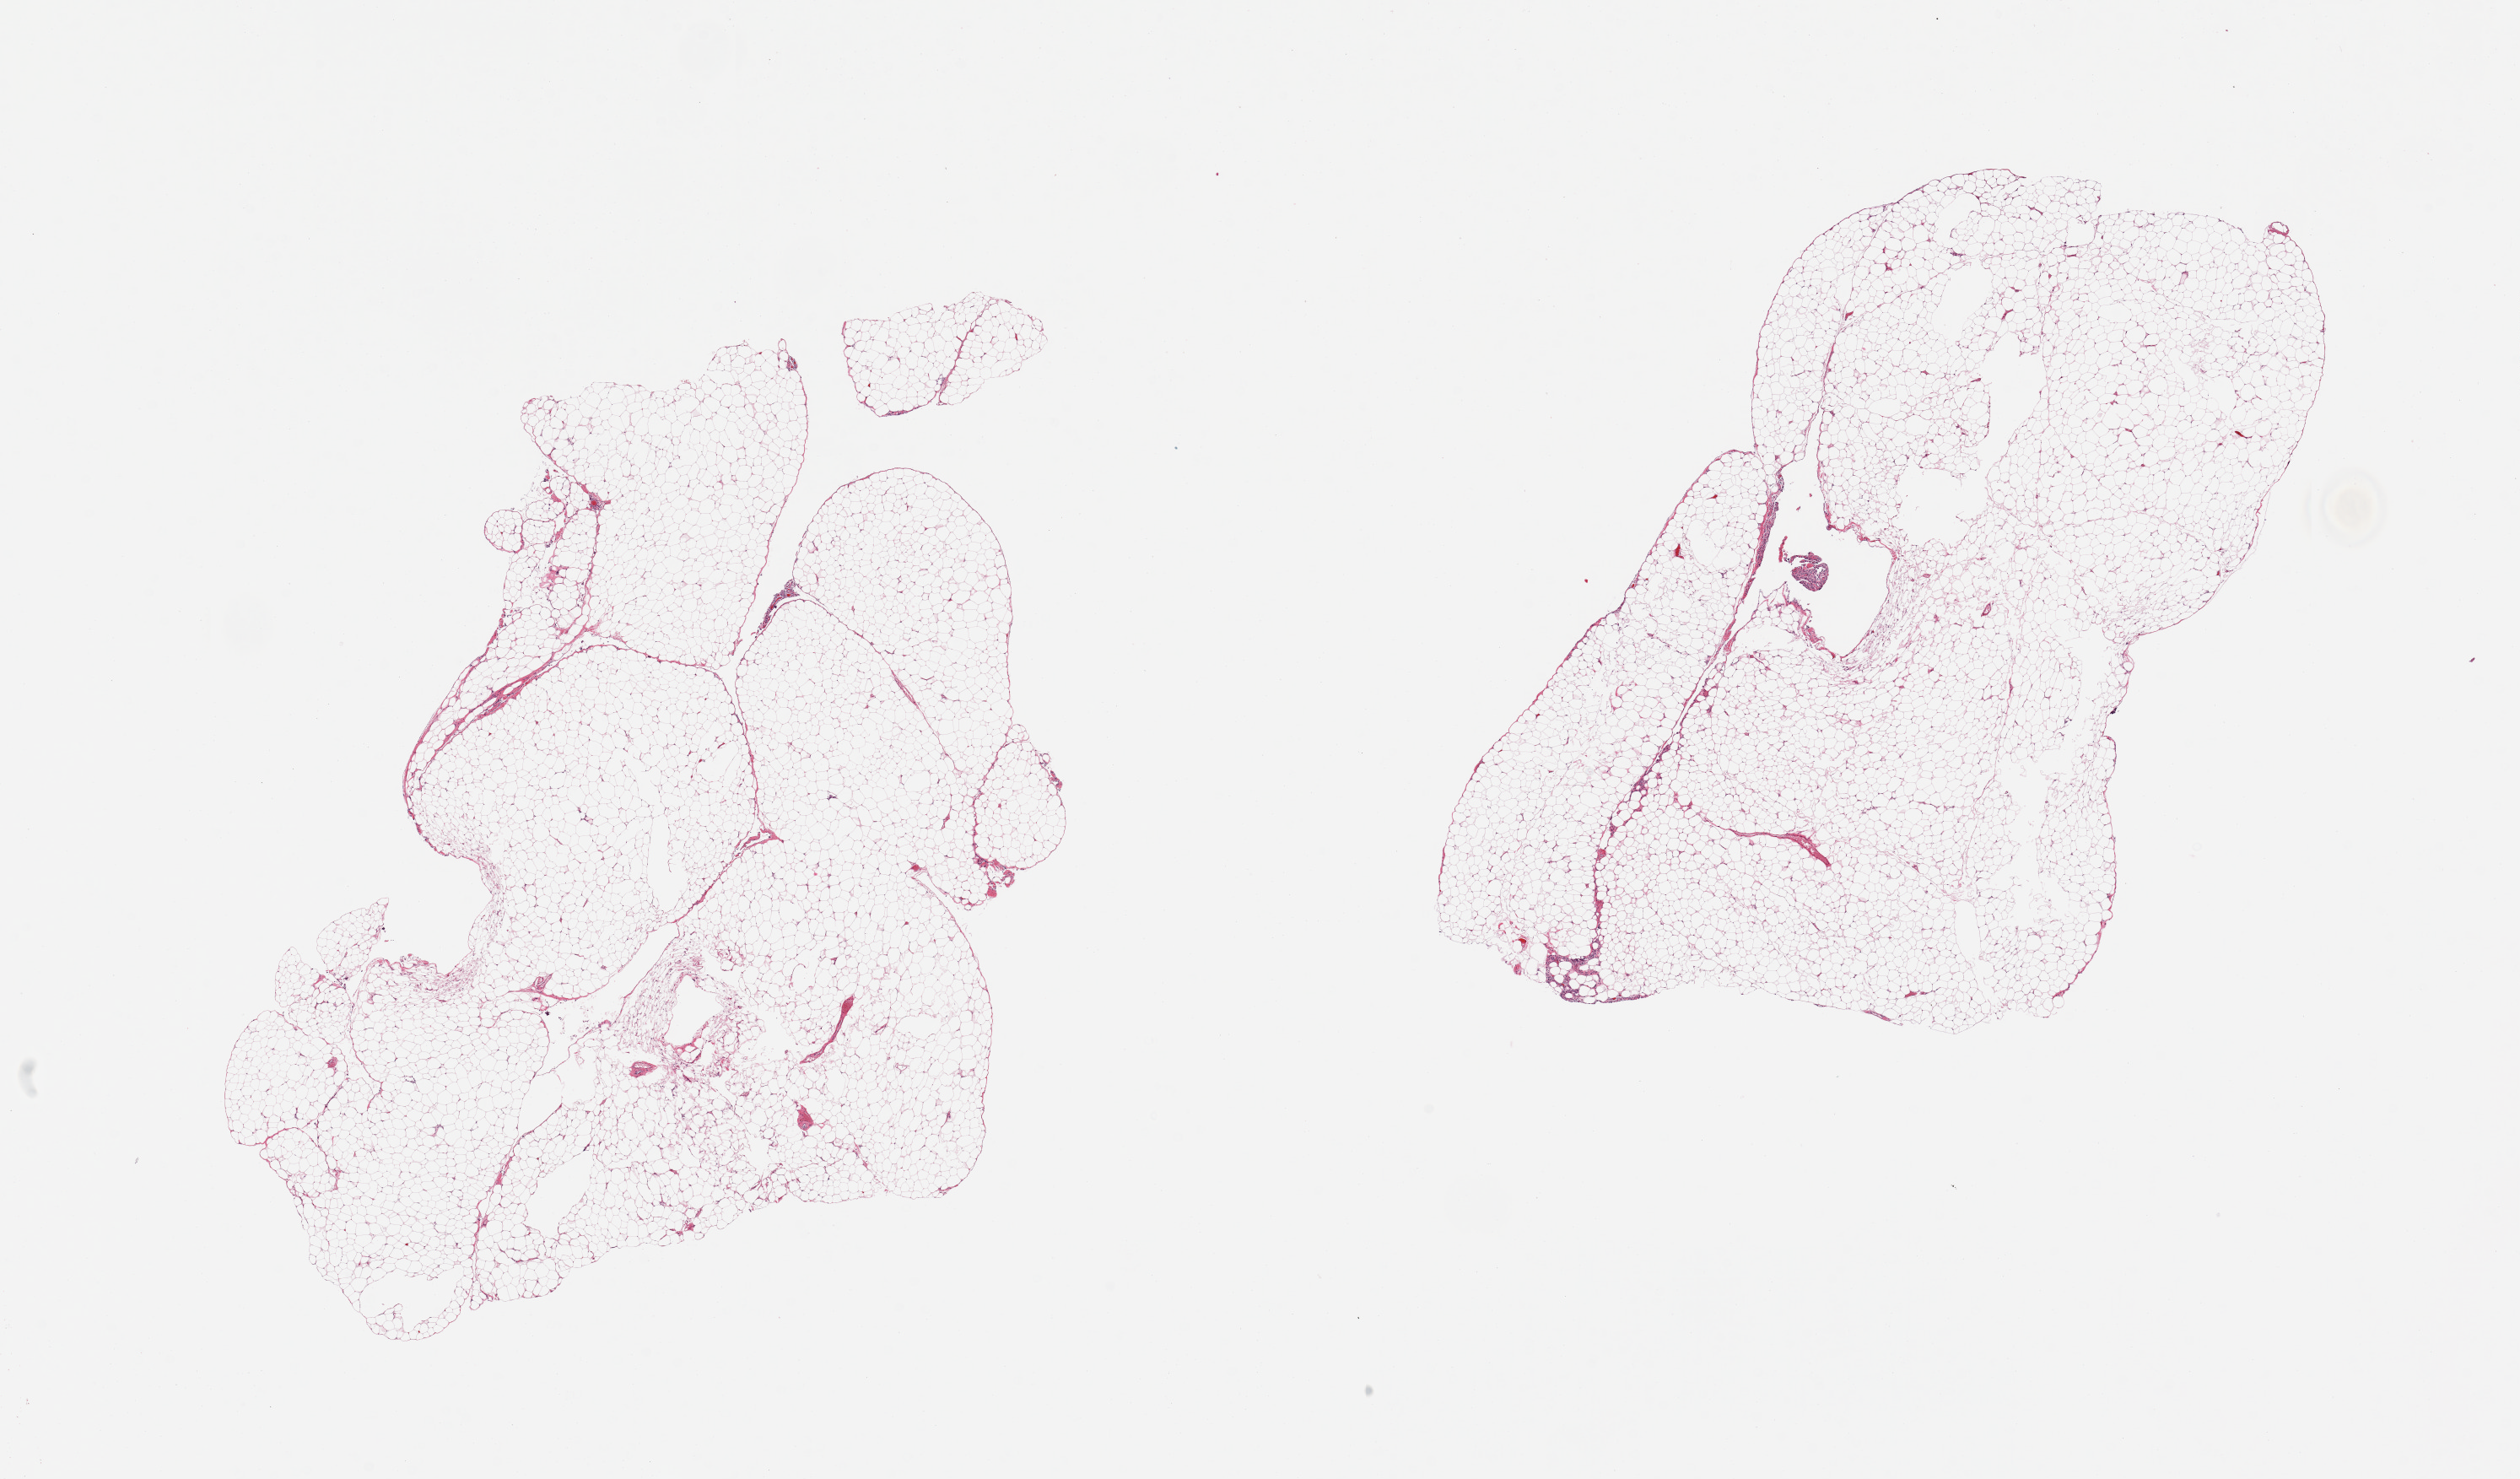
Whole-slide image, hematoxylin and eosin (H&E) stain, a low-resolution overview of the entire scanned area, about 23.6 x 13.9 mm; PAXgene-fixed, paraffin-embedded tissue; sampled site (target tissue): omentum; donor tissue sample. Donor: male.
Reviewer comment on this tissue sample: 2 pieces, trace fascia/vascular elements (<5%).